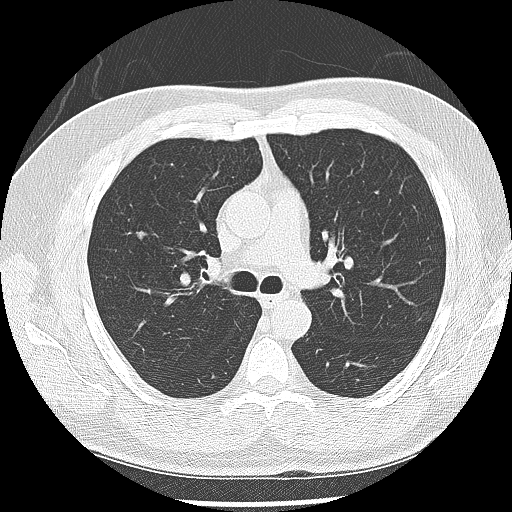
Low-dose screening chest CT, one axial slice. Reconstruction kernel LUNG. Lung window (W 1500 / L -600 HU). 2.5 mm slice thickness. 512 × 512 image matrix.
Annotated regions visible in this slice (manually delineated by an expert):
- lesion 1 (tumor, upper lobe of right lung): bounding box <136,231,147,239> (left, top, right, bottom; pixels)